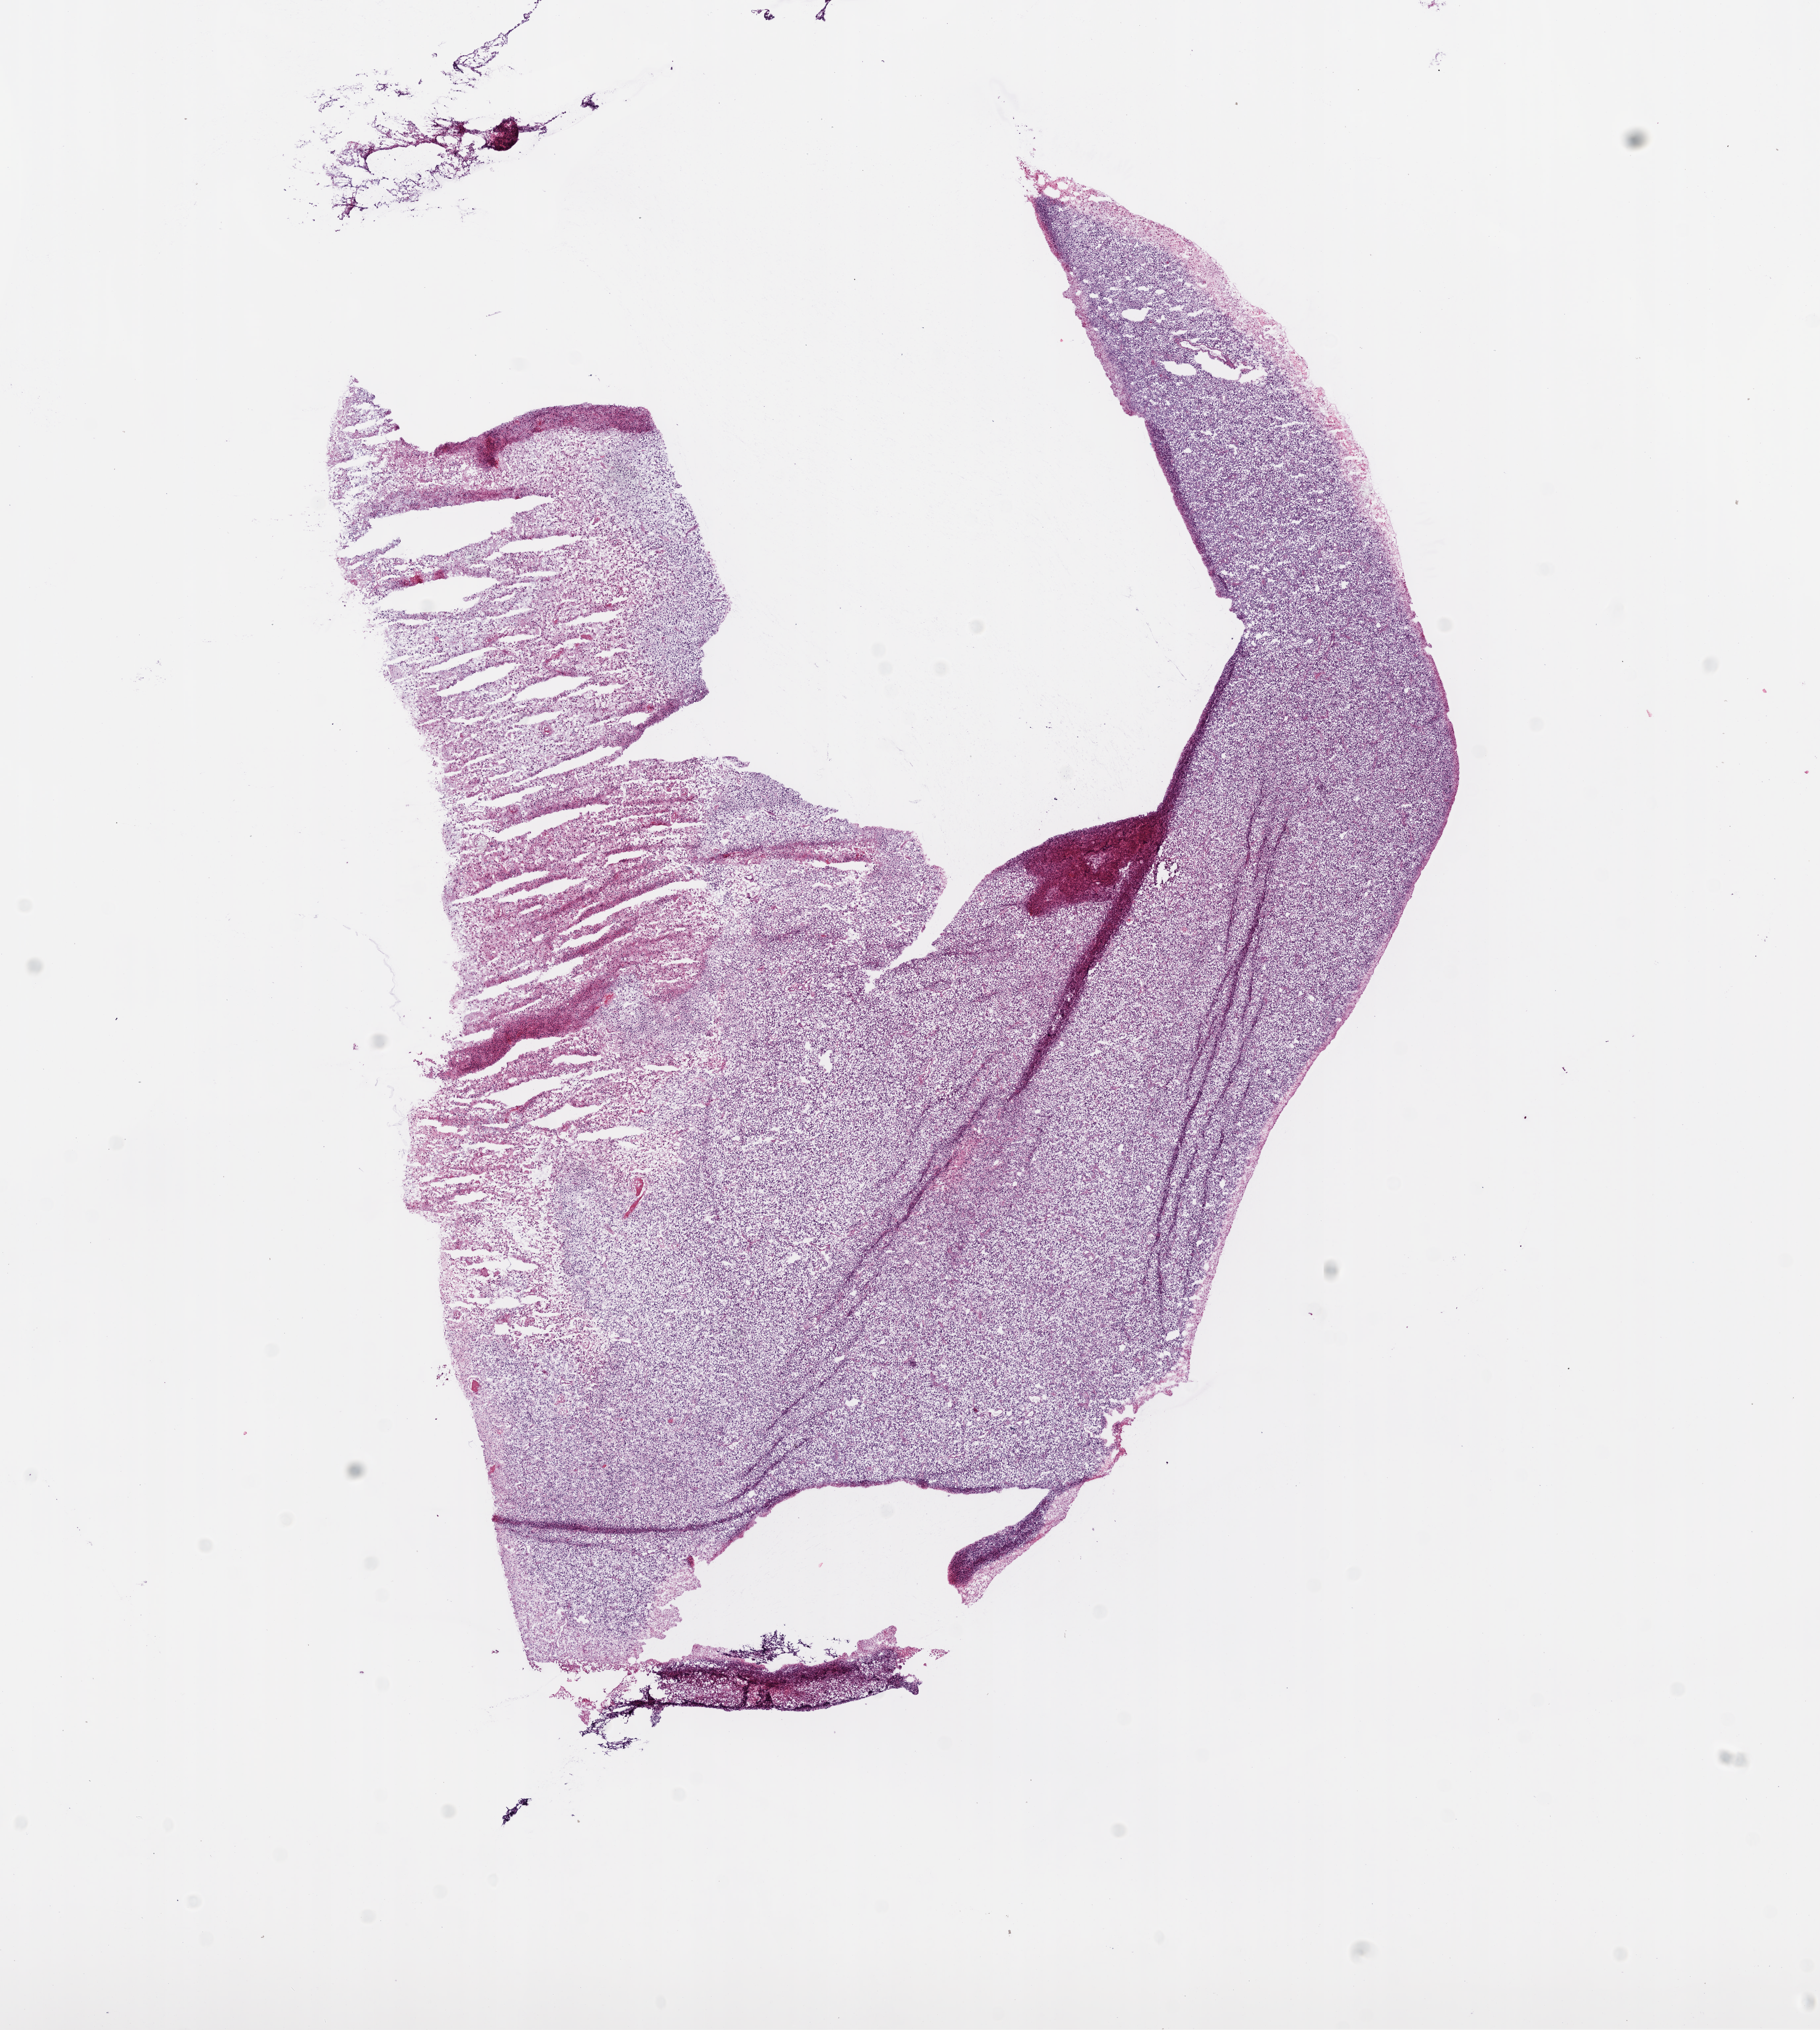
Digitized H&E tissue section (whole slide), whole scanned area (about 11.0 x 12.3 mm, slide scanned at 20x) shown as a low-resolution overview; frozen section from the bottom of the tissue portion; brain, primary tumour sample. Patient: male, age at initial diagnosis 60 years. Pathologist review of this section (percent, as recorded): tumour cells 80%, tumour nuclei 85%, normal cells 0%, stromal cells 0%, necrosis 20%.
Diagnosis: Glioblastoma.